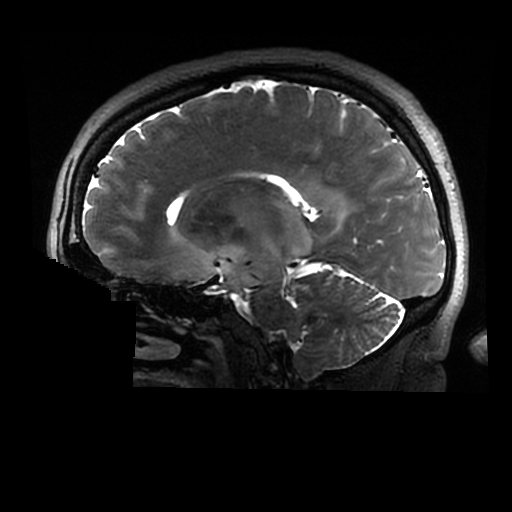
Brain MRI from a brain-tumour surgery series, one sagittal slice. Position 174 of 320 along the scan axis. 0.6 mm slice thickness. 512 × 512 image matrix, field of view 240 × 240 mm. Case-level facts recorded for this patient, not image findings: histopathology: Astrocytoma; WHO grade: 2; IDH mutation: yes.
Annotated regions visible in this slice (outlined manually by an expert reader):
- tumour: bounding box [x1, y1, x2, y2] px = [202, 200, 312, 298]